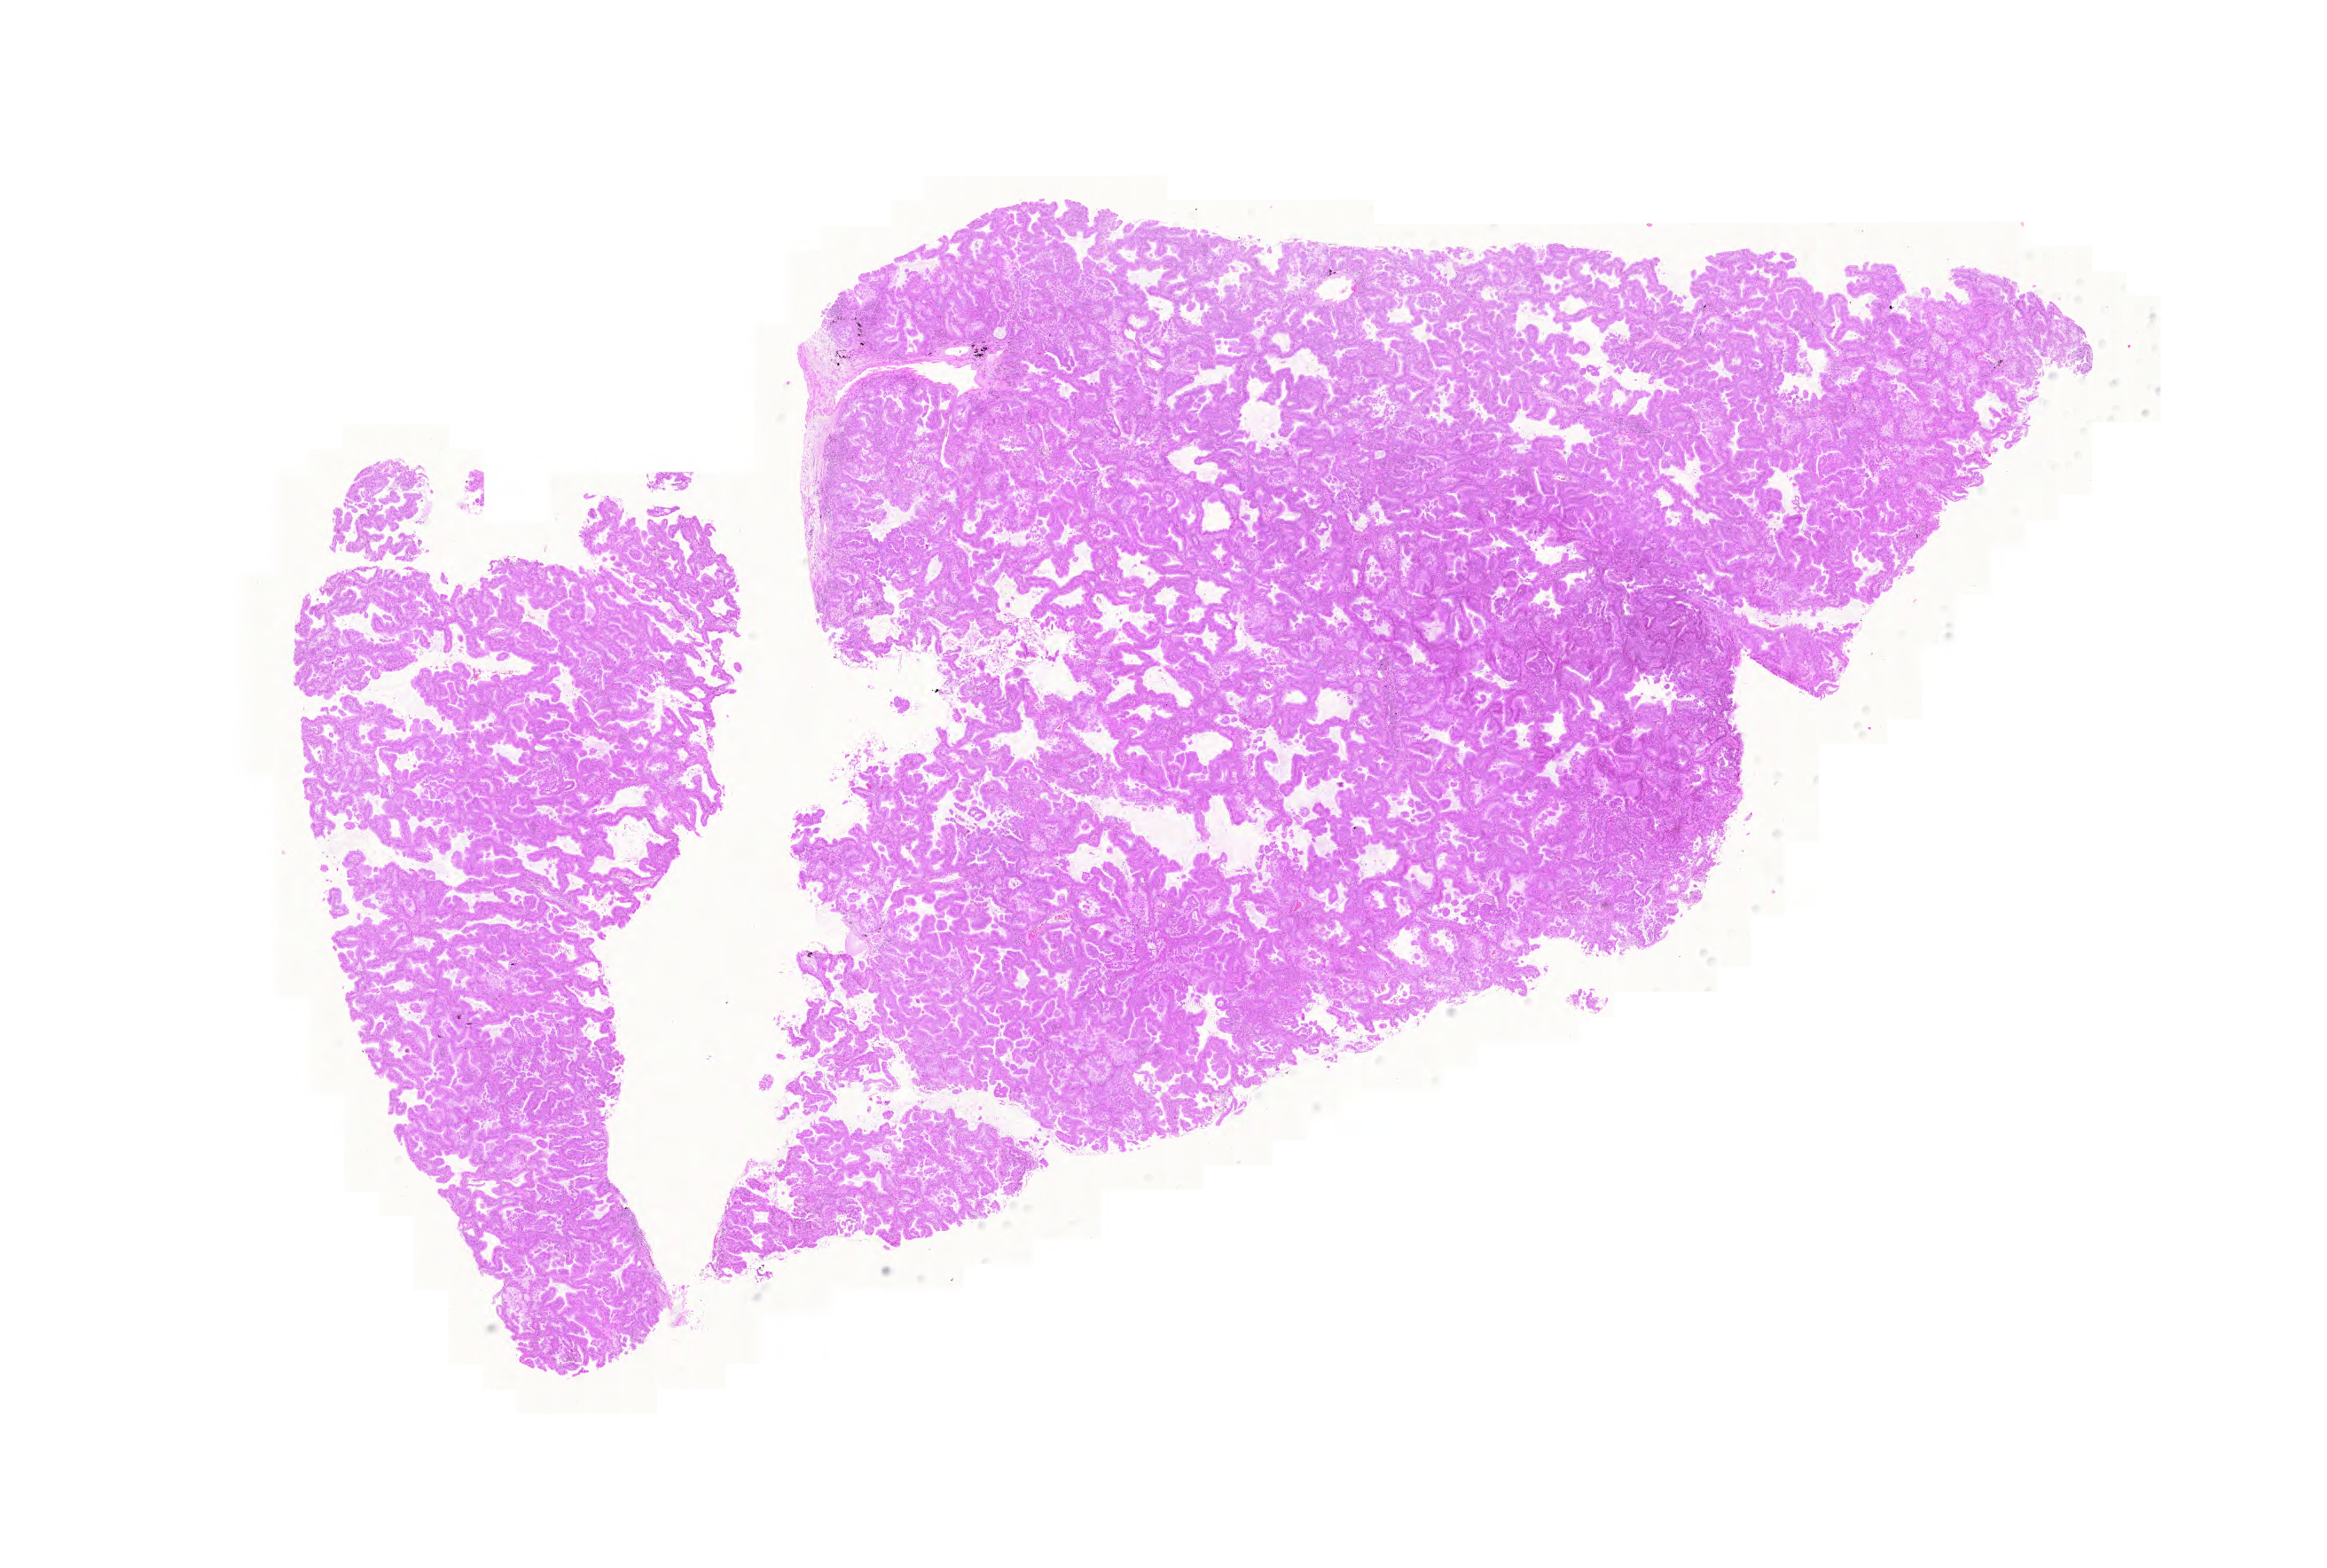
Digitized H&E tissue section (whole slide), a low-resolution overview of the entire scanned area, about 19.5 x 13.2 mm (slide scanned at 20x), formalin-fixed paraffin-embedded (FFPE) diagnostic section, primary tumour sample from the lung. Patient: male, age at initial diagnosis 76 years.
• laterality: right
• pathologic diagnosis: Adenocarcinoma with mixed subtypes (lower lobe, lung)
• TNM: T4 N1 M0
• AJCC pathologic stage: IIIB (5th edition)